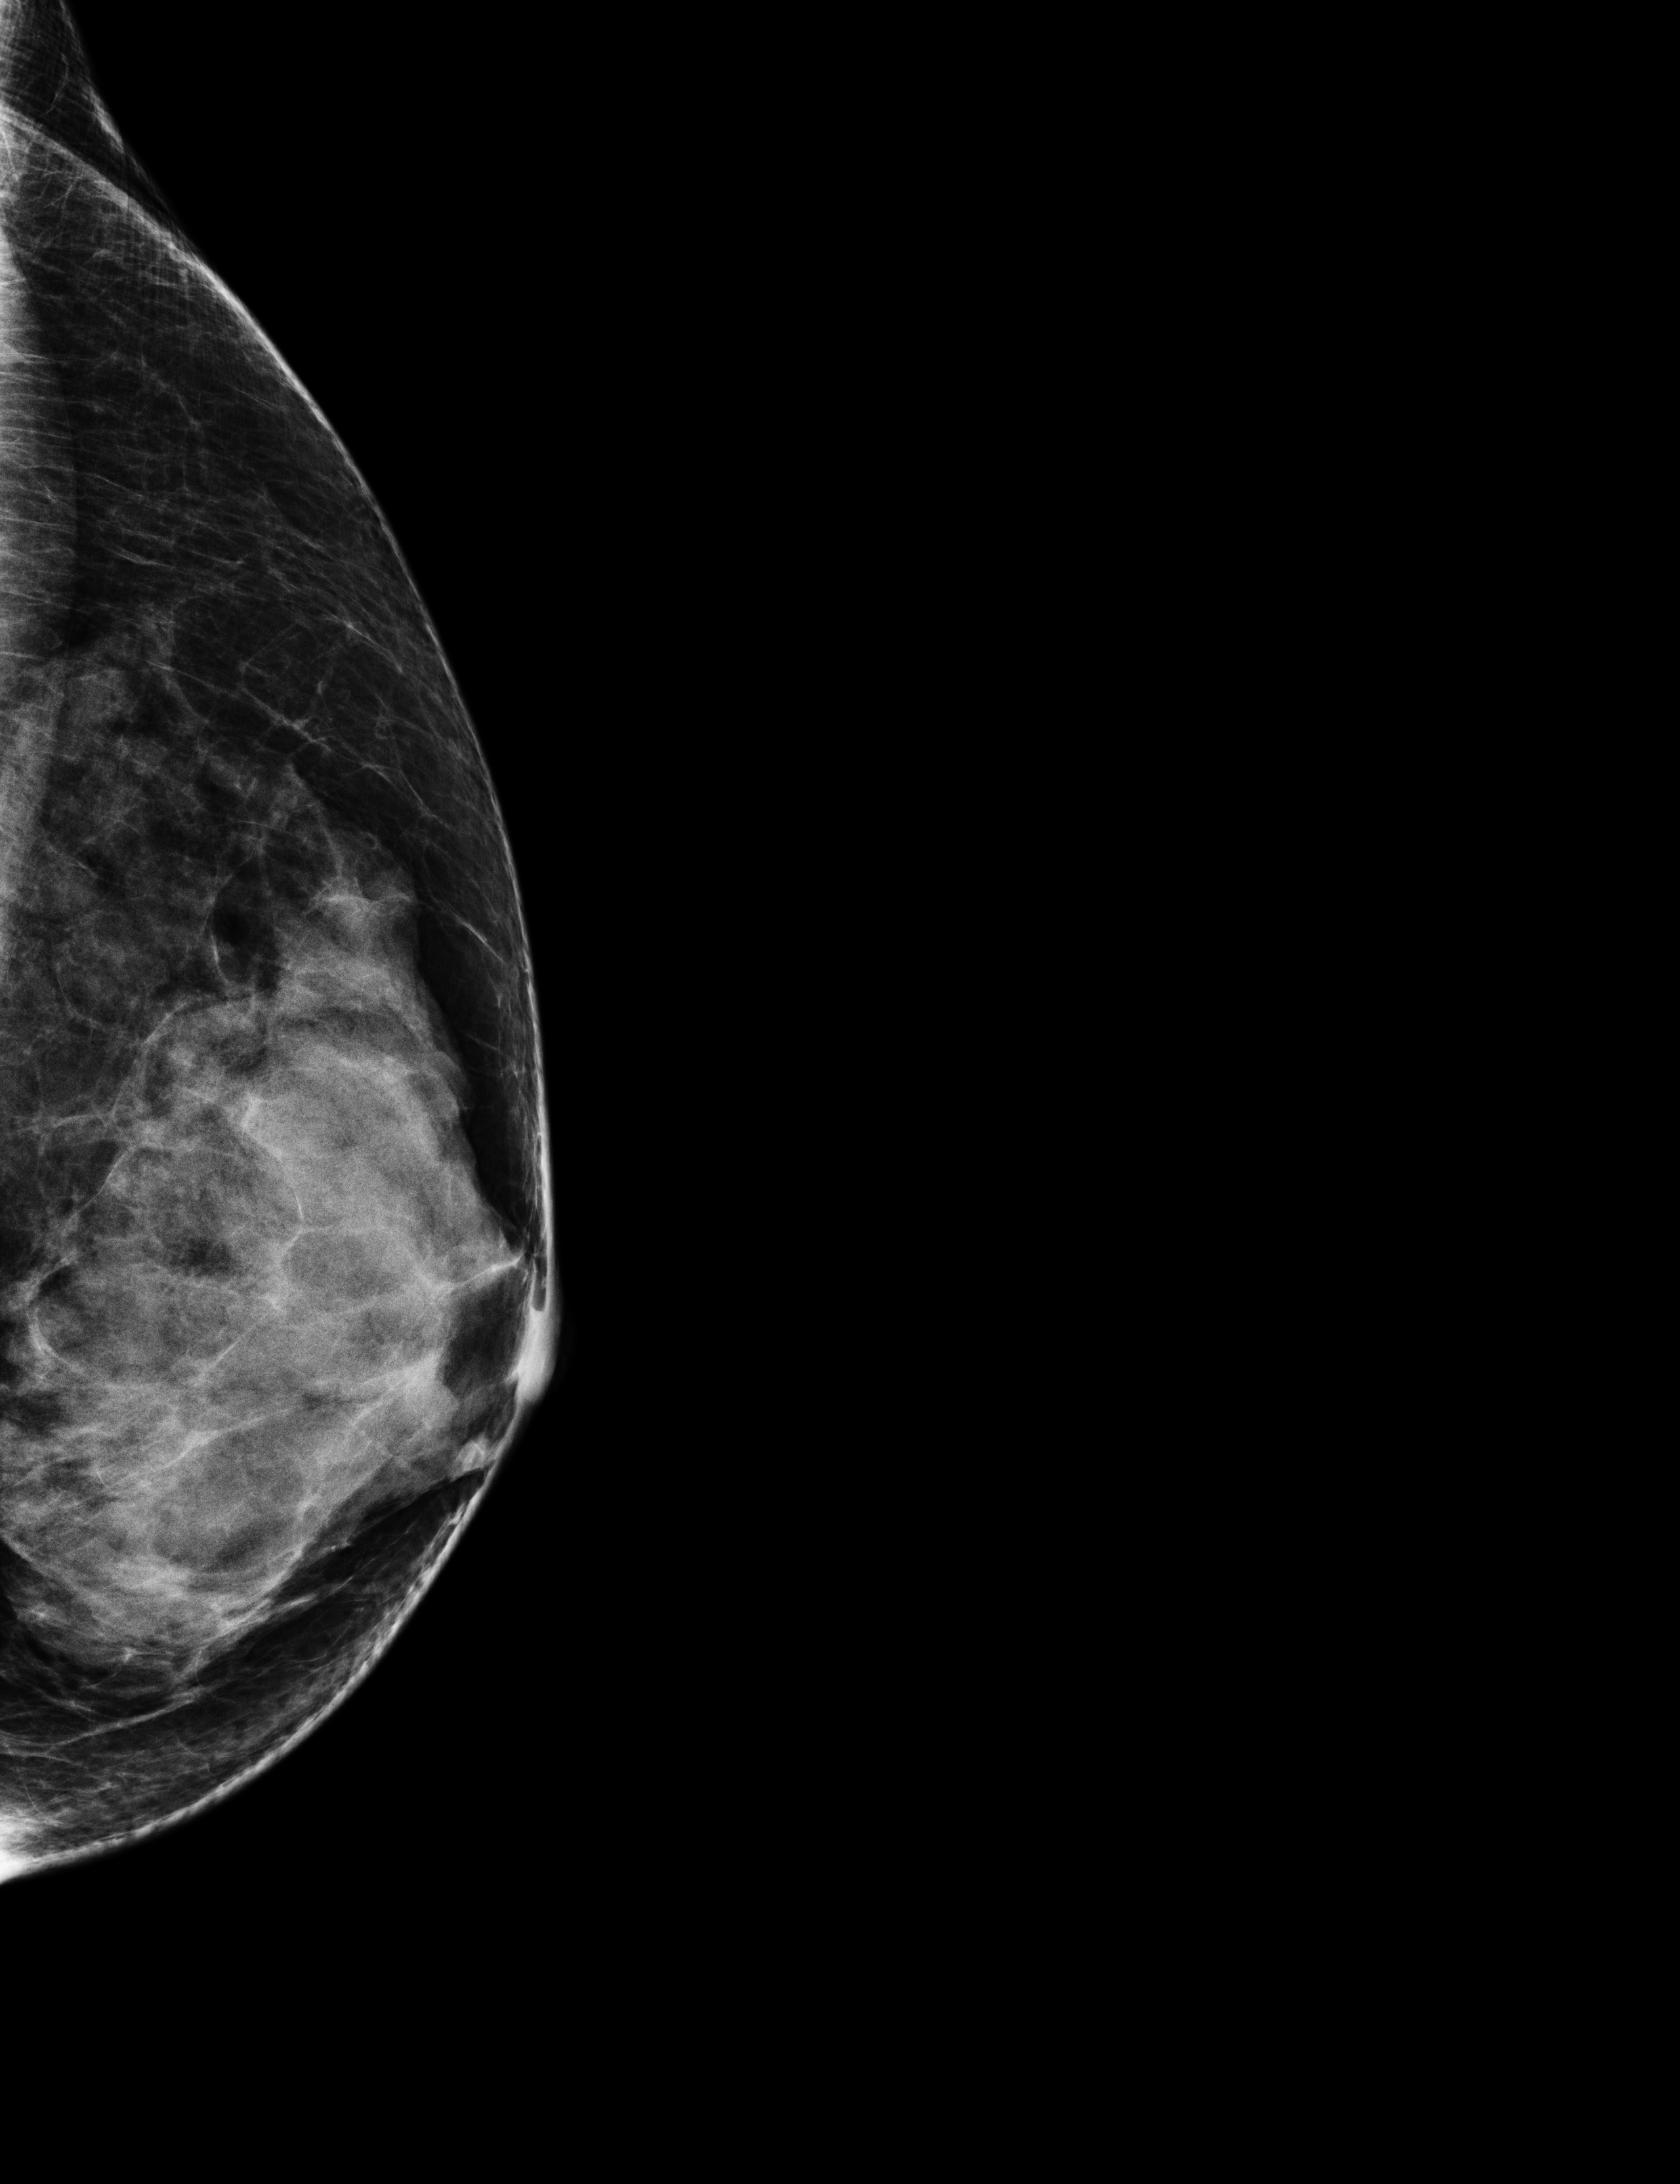
Screening examination. Patient: female, 66 years.
Image type: full-field digital mammogram. Breast: left. Projection: exaggerated CC view (lateral).